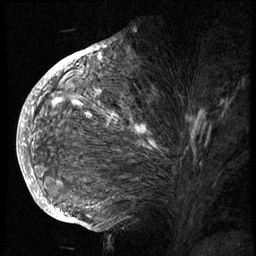
Breast MRI (dynamic contrast-enhanced), one sagittal slice; slice 40 of 74 in the series (ordered by position); 3 images stored at this slice position (order not interpretable as contrast timing); 1.5 T; TE 4.2 ms, TR 8.9 ms; 2.5 mm slice thickness; 256 × 256 image matrix, field of view 200 × 200 mm. Patient: female, 57 years. Case-level facts recorded for this patient, not image findings: setting: breast cancer imaged before/during neoadjuvant chemotherapy; receptor status: HER2-positive.
Annotated regions visible in this slice (semi-automatically segmented with operator editing):
- analysis volume of interest (the breast-tissue region the enhancement analysis was run in; not a lesion): box from (x=40, y=62) to (x=238, y=175) px
- tumour enhancement mask (voxels above the 140 % enhancement threshold inside the analysis volume of interest): (x=52, y=91)–(x=155, y=149)